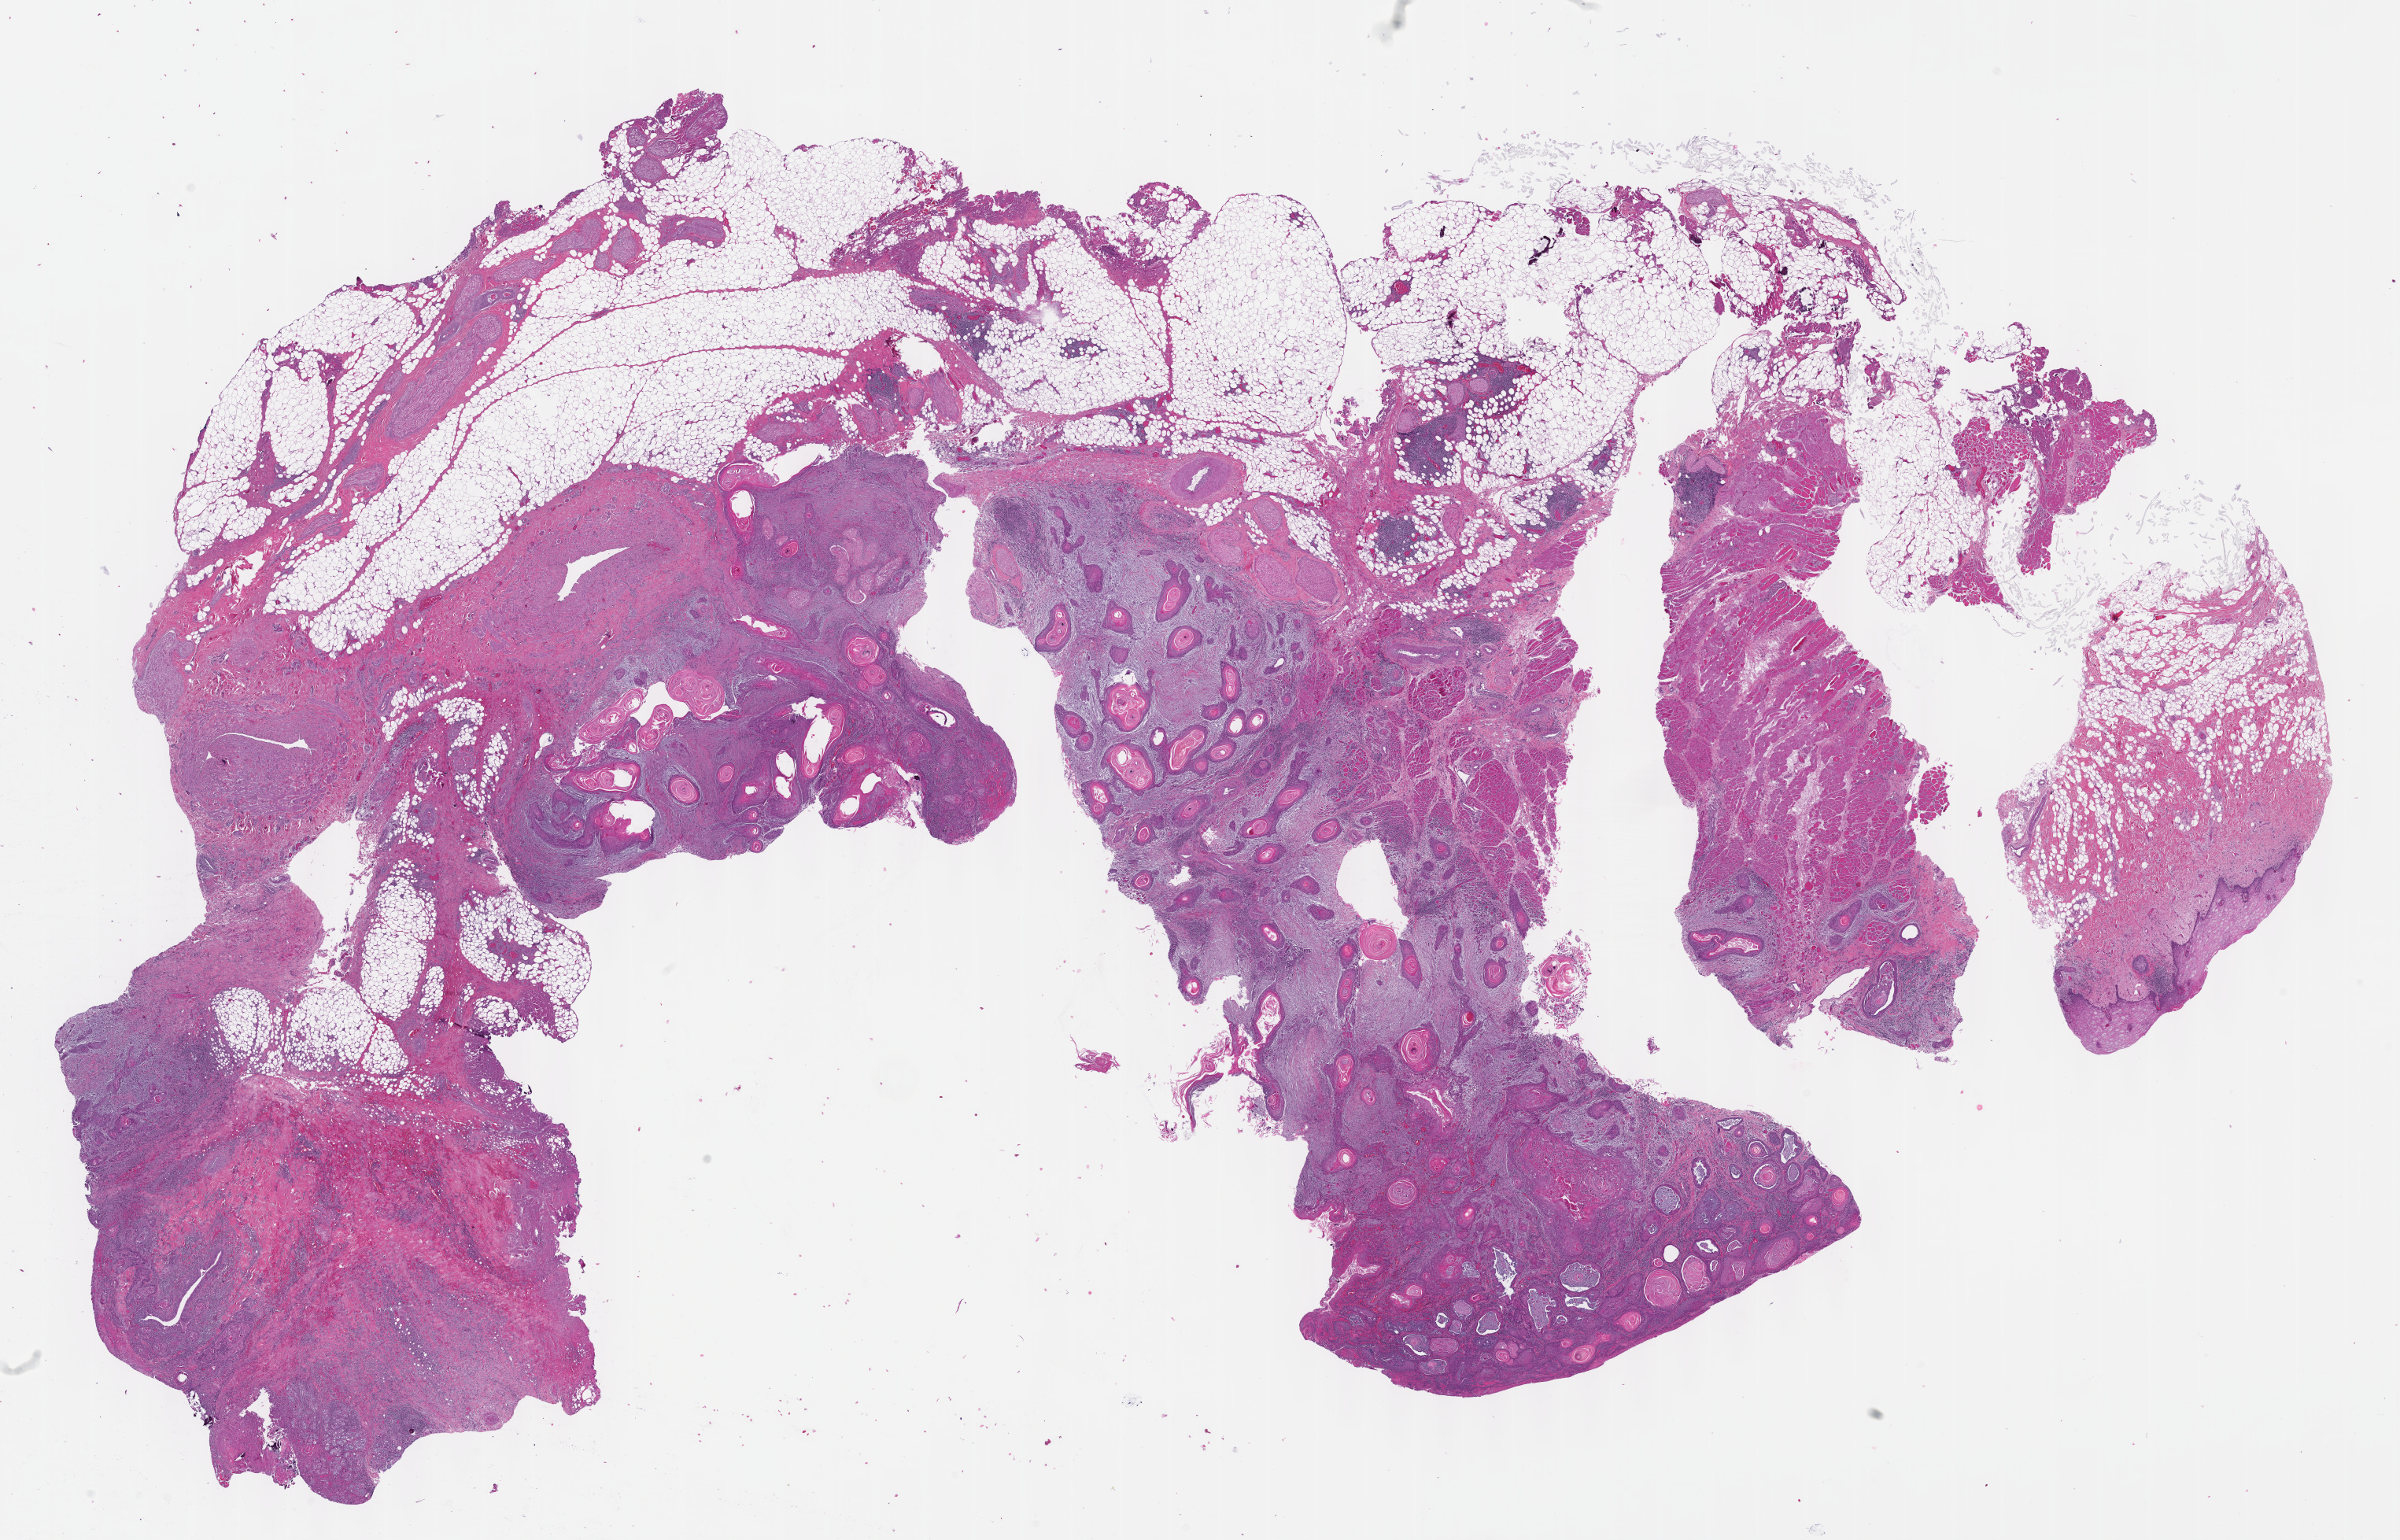
H&E whole-slide image — whole scanned area (about 24.6 x 15.8 mm, from a 40x scan) shown as a low-resolution overview, formalin-fixed paraffin-embedded (FFPE) diagnostic section, head and neck, primary tumour sample. Male patient; age at initial diagnosis 48 years. Histologic grade: G2 (moderately differentiated).
- AJCC pathologic stage: III
- laterality: left
- TNM: T3 N0 M0
- diagnosis: Squamous cell carcinoma, NOS (cheek mucosa)